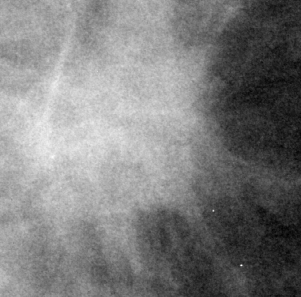
Region of interest cut from a scanned film mammogram (one marked finding), right breast, CC view.
Finding: mass, shape irregular / architectural distortion, margins spiculated; BI-RADS assessment category 4; pathology (as recorded): malignant.